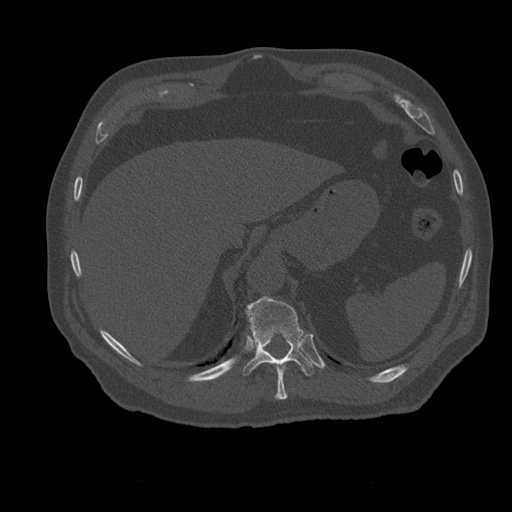
CT including the spine, one axial slice; slice 285 of 399 in the series (ordered by position); reconstruction kernel STANDARD; bone window (W 1800 / L 400 HU); 1.25 mm slice thickness; 512 × 512 image matrix, field of view 407 × 407 mm. Patient age 73 years. From the clinical record (not read from this slice): primary cancer: prostate; vertebrae with lytic lesions (as recorded): L2.
Outlined on this slice (semi-automatic segmentation, software-assisted and operator-edited):
- T10 vertebra: box from (x=275, y=363) to (x=288, y=400) px
- T11 vertebra: (x=243, y=296)–(x=315, y=376)